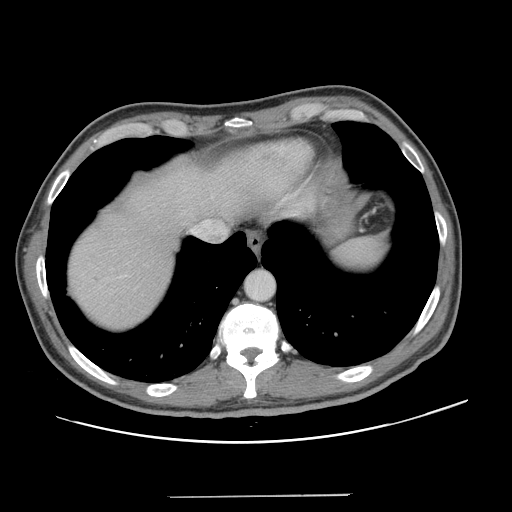
Contrast-enhanced abdominal CT, one axial slice. Position 116 of 131 along the scan axis. 120 kVp. Intravenous contrast given. Soft-tissue window (W 400 / L 40 HU). 2.5 mm slice thickness. 512 × 512 image matrix. Male patient, age 60 years. From the clinical record (not read from this slice): diagnosis: colorectal cancer liver metastases, imaged before liver resection.
Outlined on this slice (manually delineated by an expert):
- hepatic veins: bounding box <190,220,216,239> (left, top, right, bottom; pixels)
- liver: <67,142,308,332>
- planned liver remnant (the part of the liver to remain after resection): <66,144,308,329>